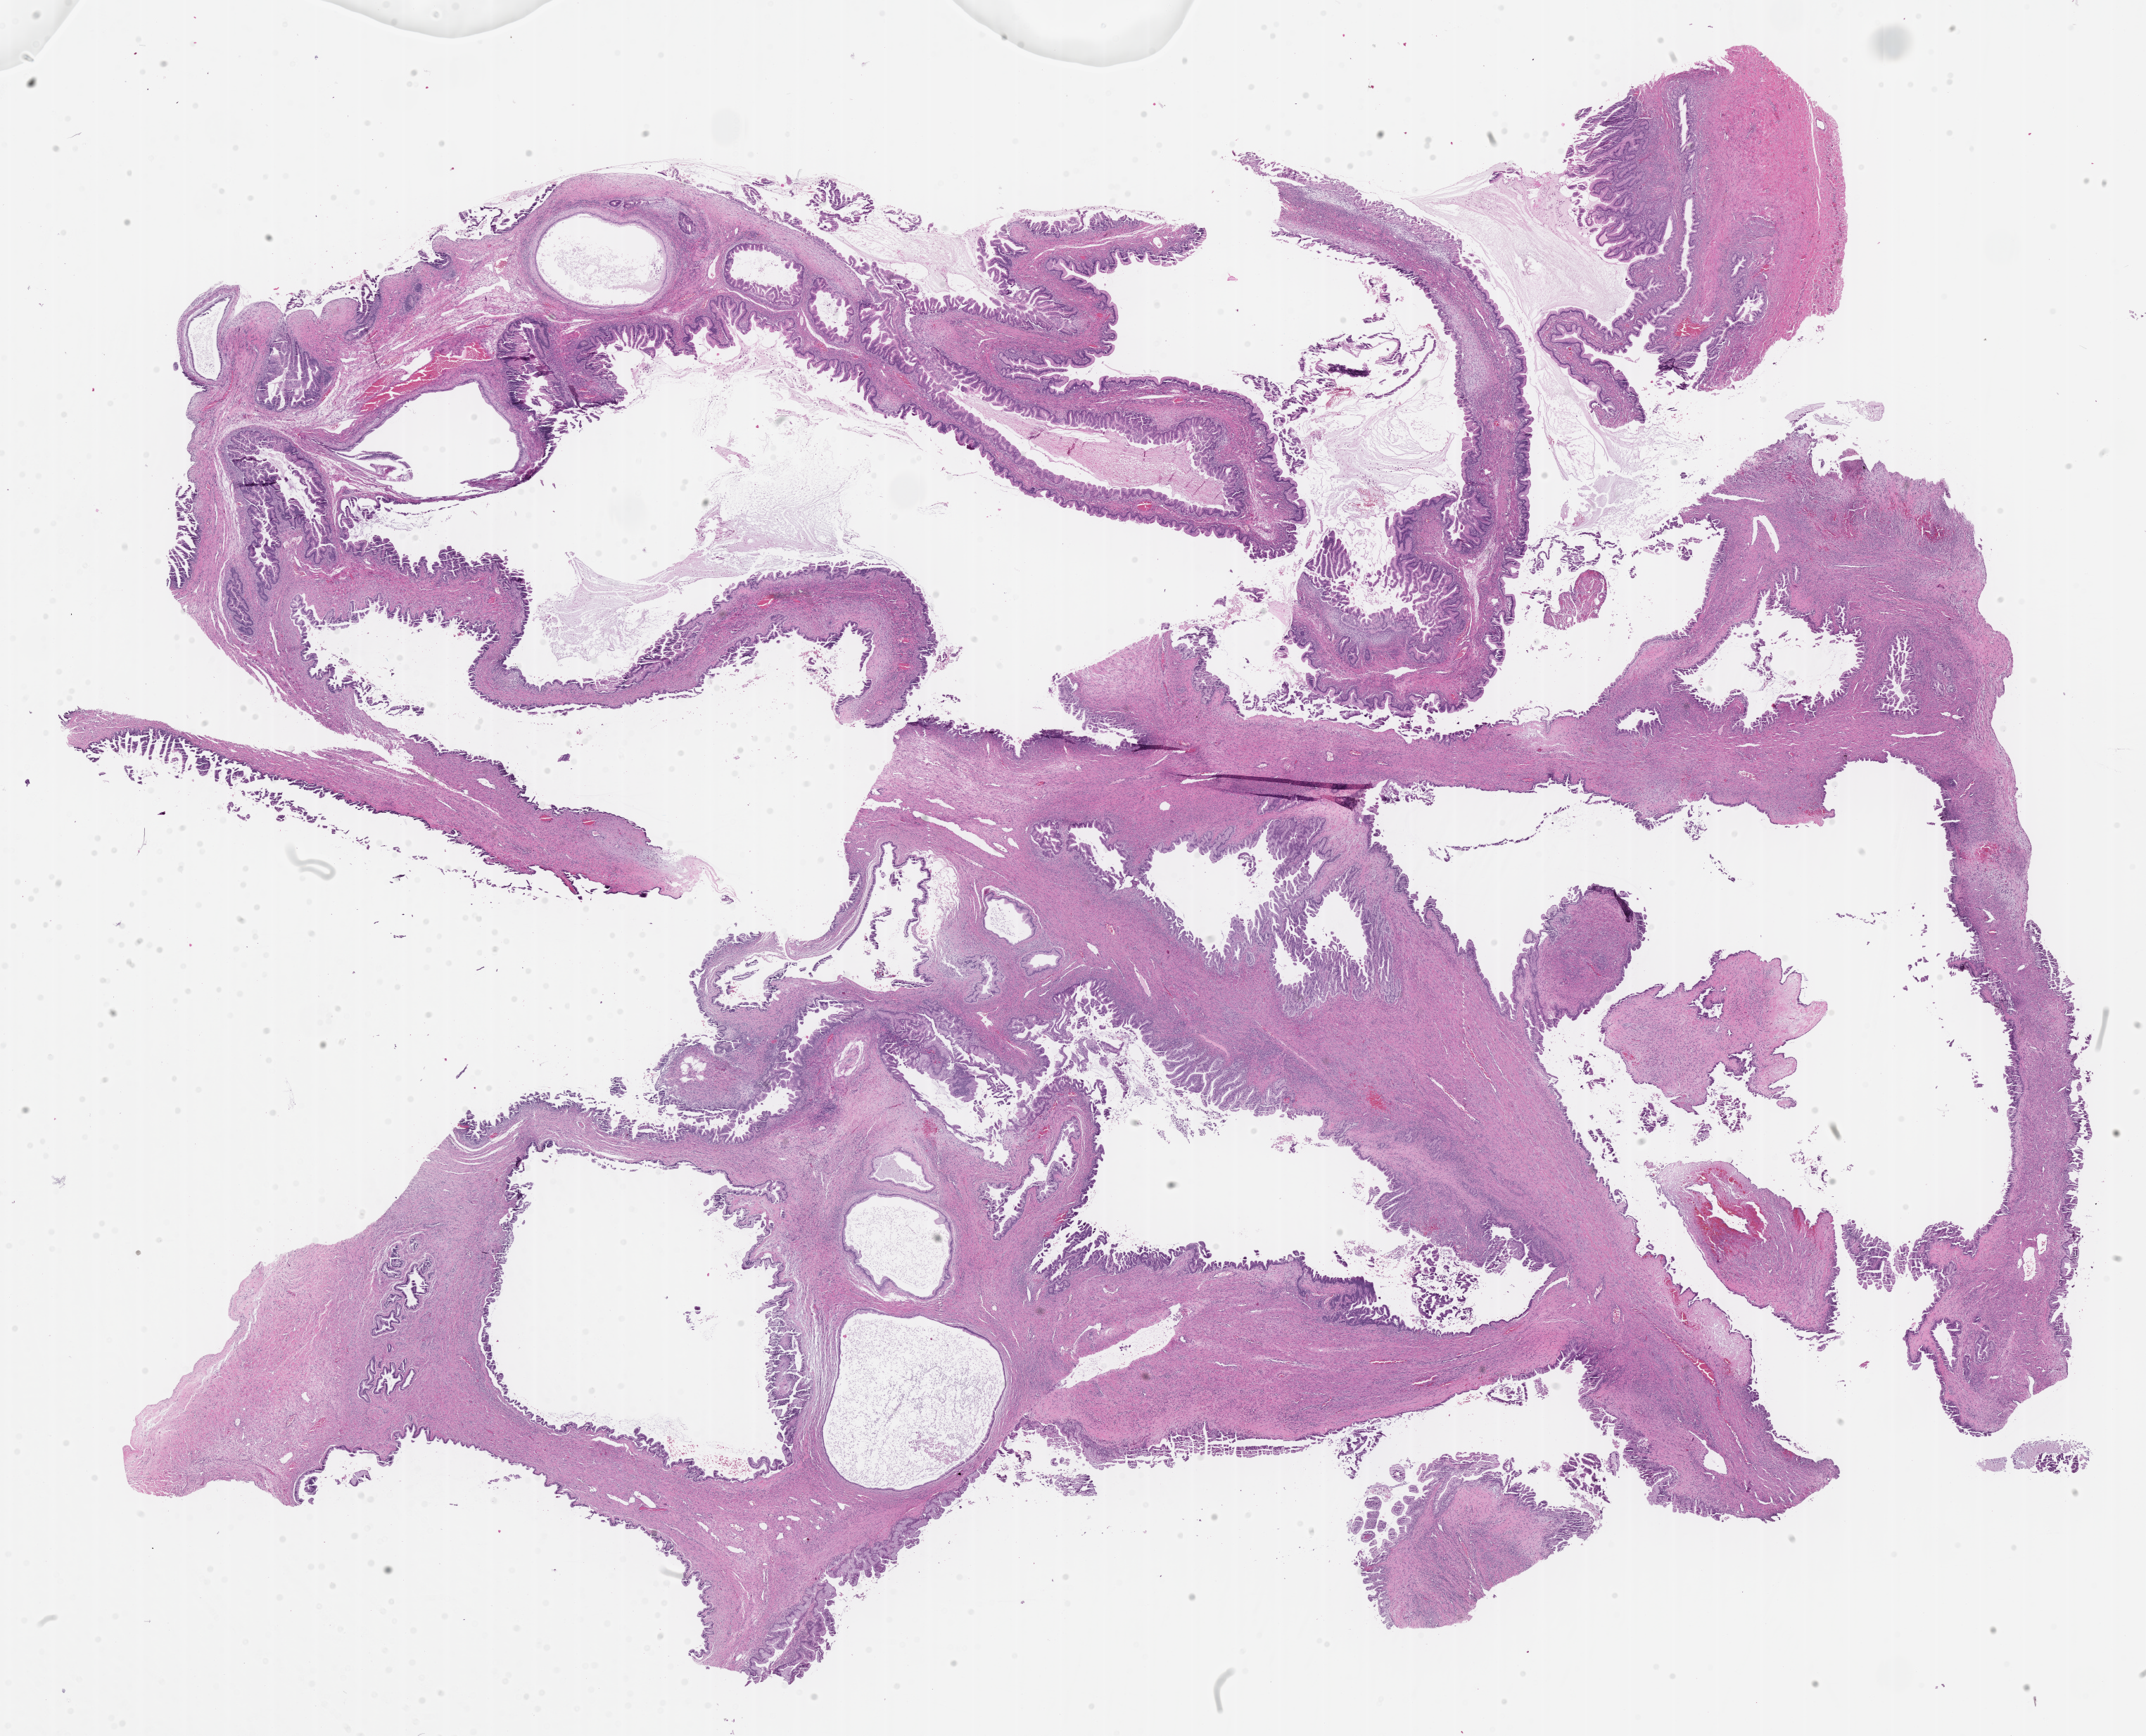
Whole-slide image, haematoxylin and eosin stain — whole scanned area (about 24.6 x 19.9 mm) shown as a low-resolution overview. Formalin-fixed, paraffin-embedded (FFPE) tissue. Specimen: primary tumor. Site: ovary (right). Female, age 72 years at initial diagnosis. Slide review estimates, as recorded: tumor cells 30%, tumor nuclei 40%, stromal cells 70%, necrosis 0%, normal cells 0%. Inflammatory infiltration, as recorded: lymphocyte infiltration 0%, monocyte infiltration 0%, neutrophil infiltration 0%.
Section: top of the tissue portion. FIGO stage: Stage IC2. Histologic diagnosis: Mucinous adenocarcinoma.